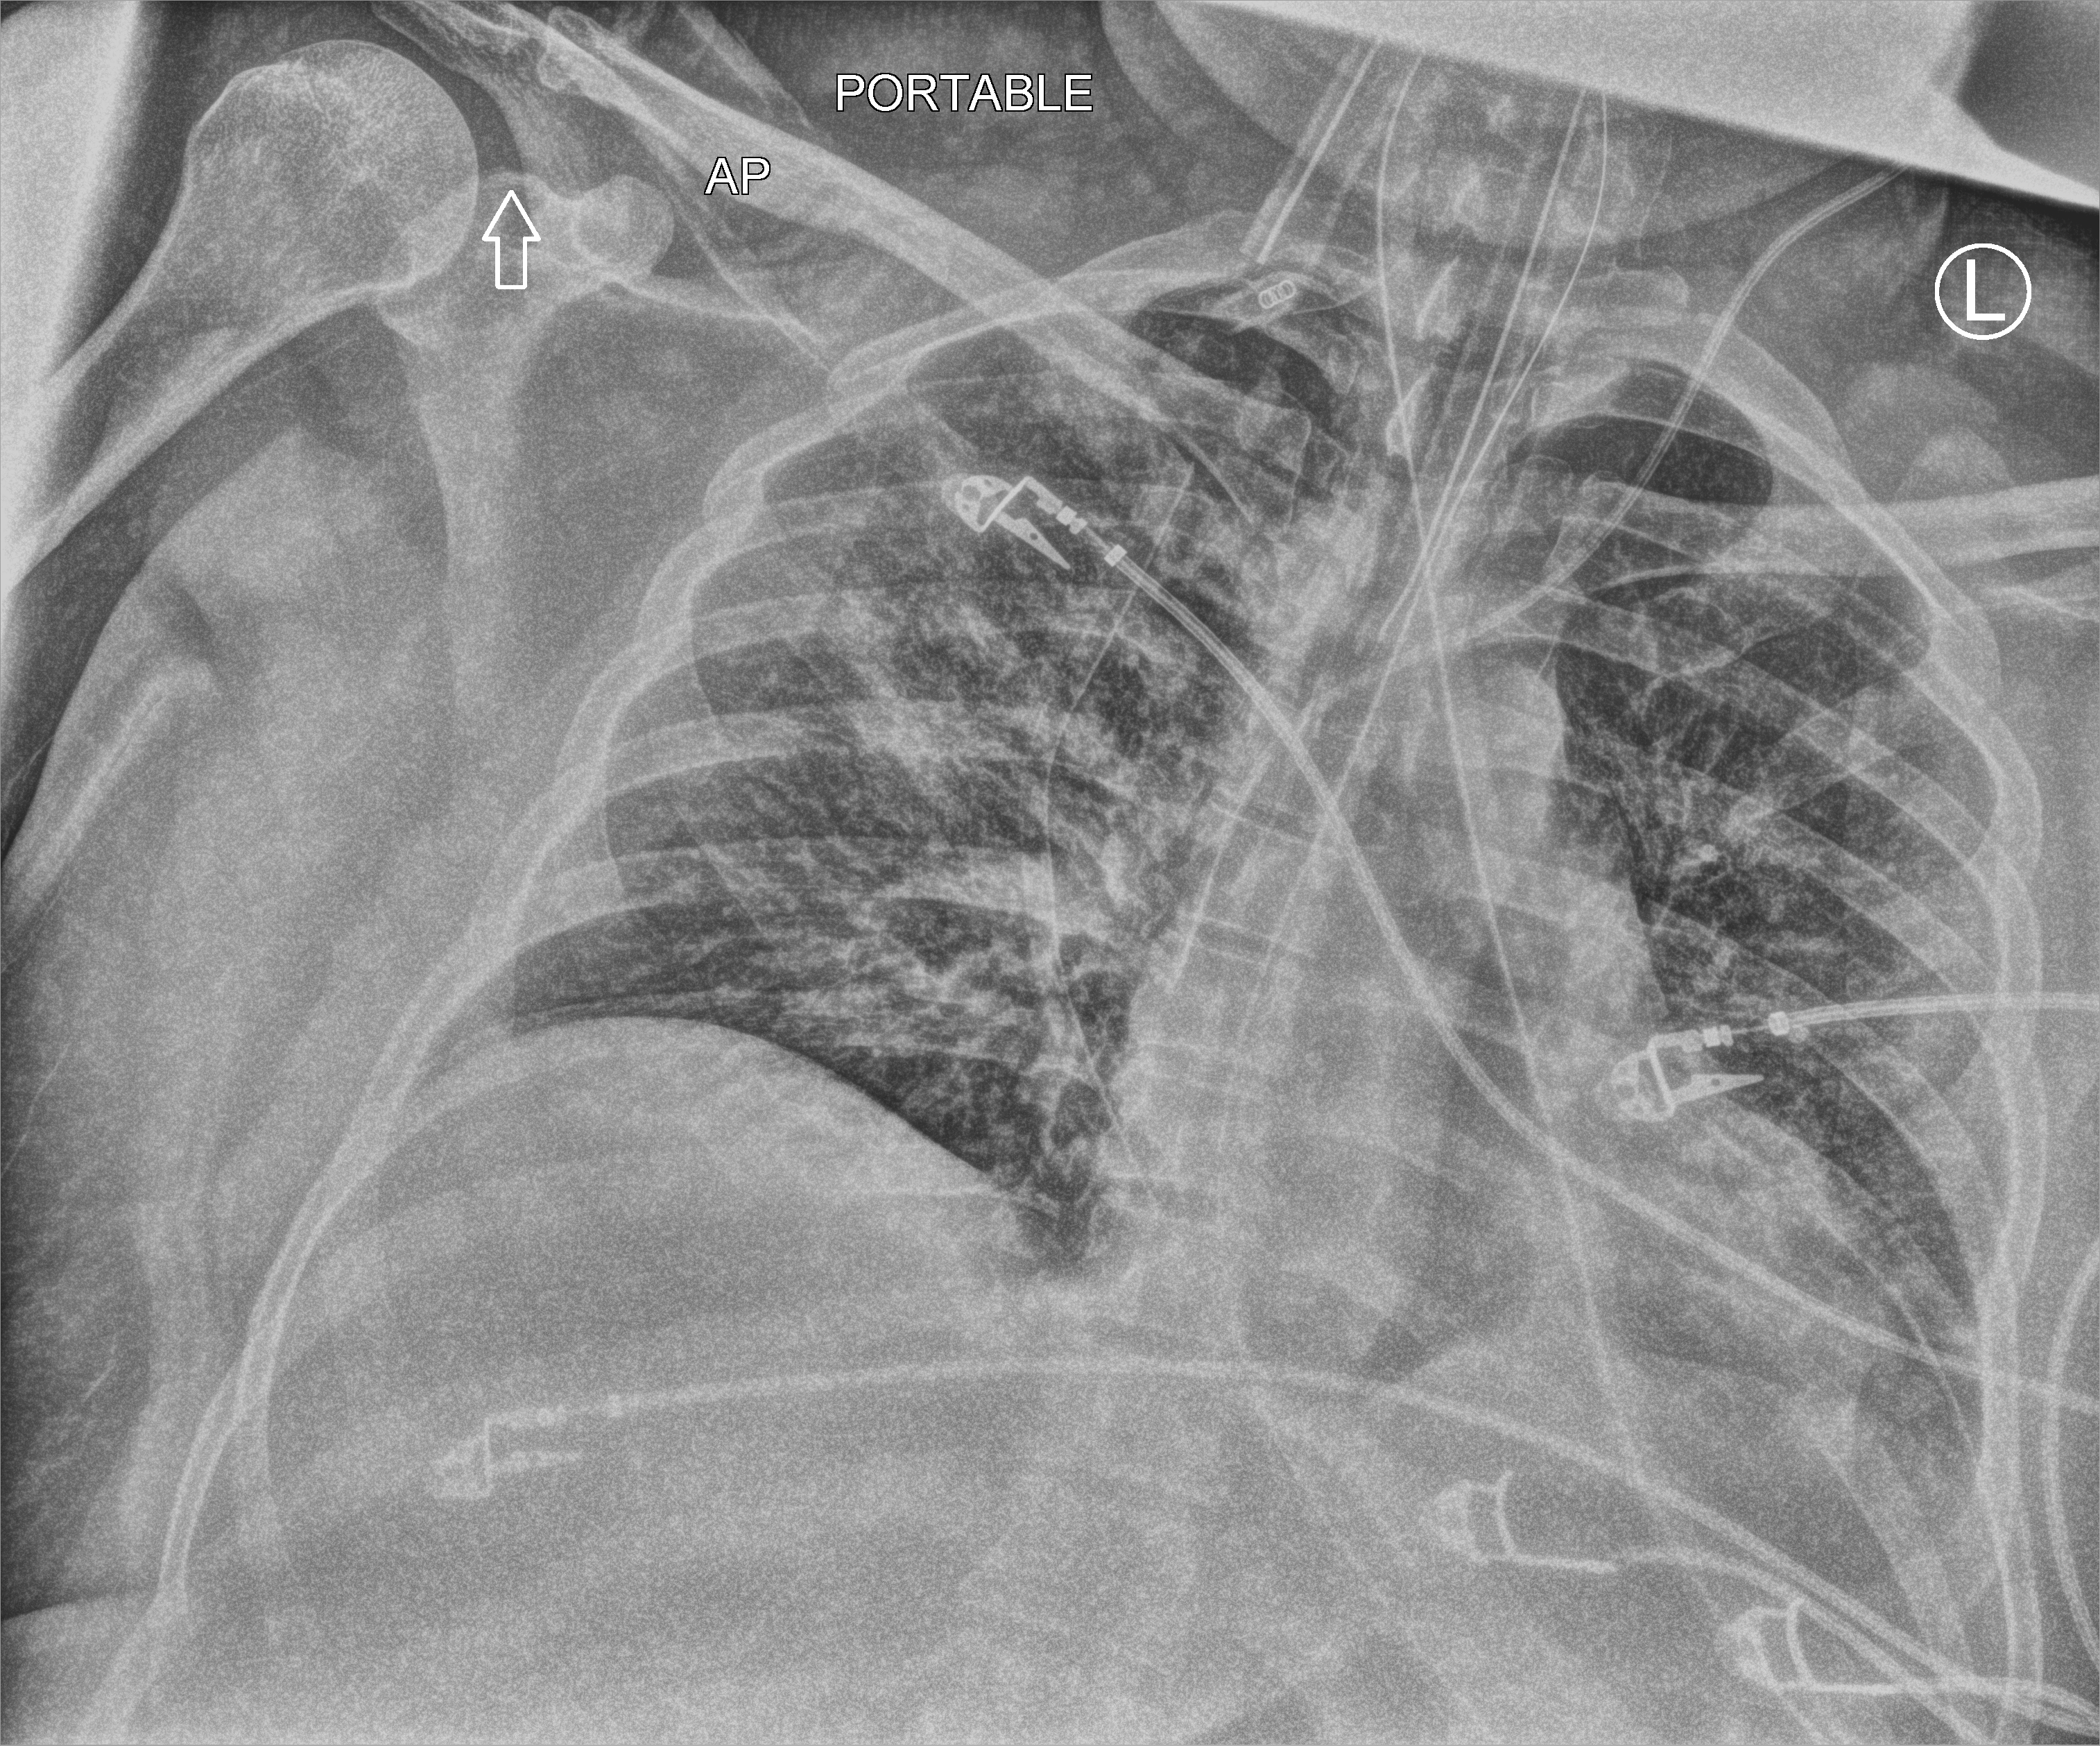
Portable chest radiograph. Patient hospitalised with COVID-19, aged 18–59 years.
Admission-level facts for this patient (not findings on this image; timing relative to this image not recorded):
- mechanically ventilated during this hospital stay: yes
- diabetes (admission record): no